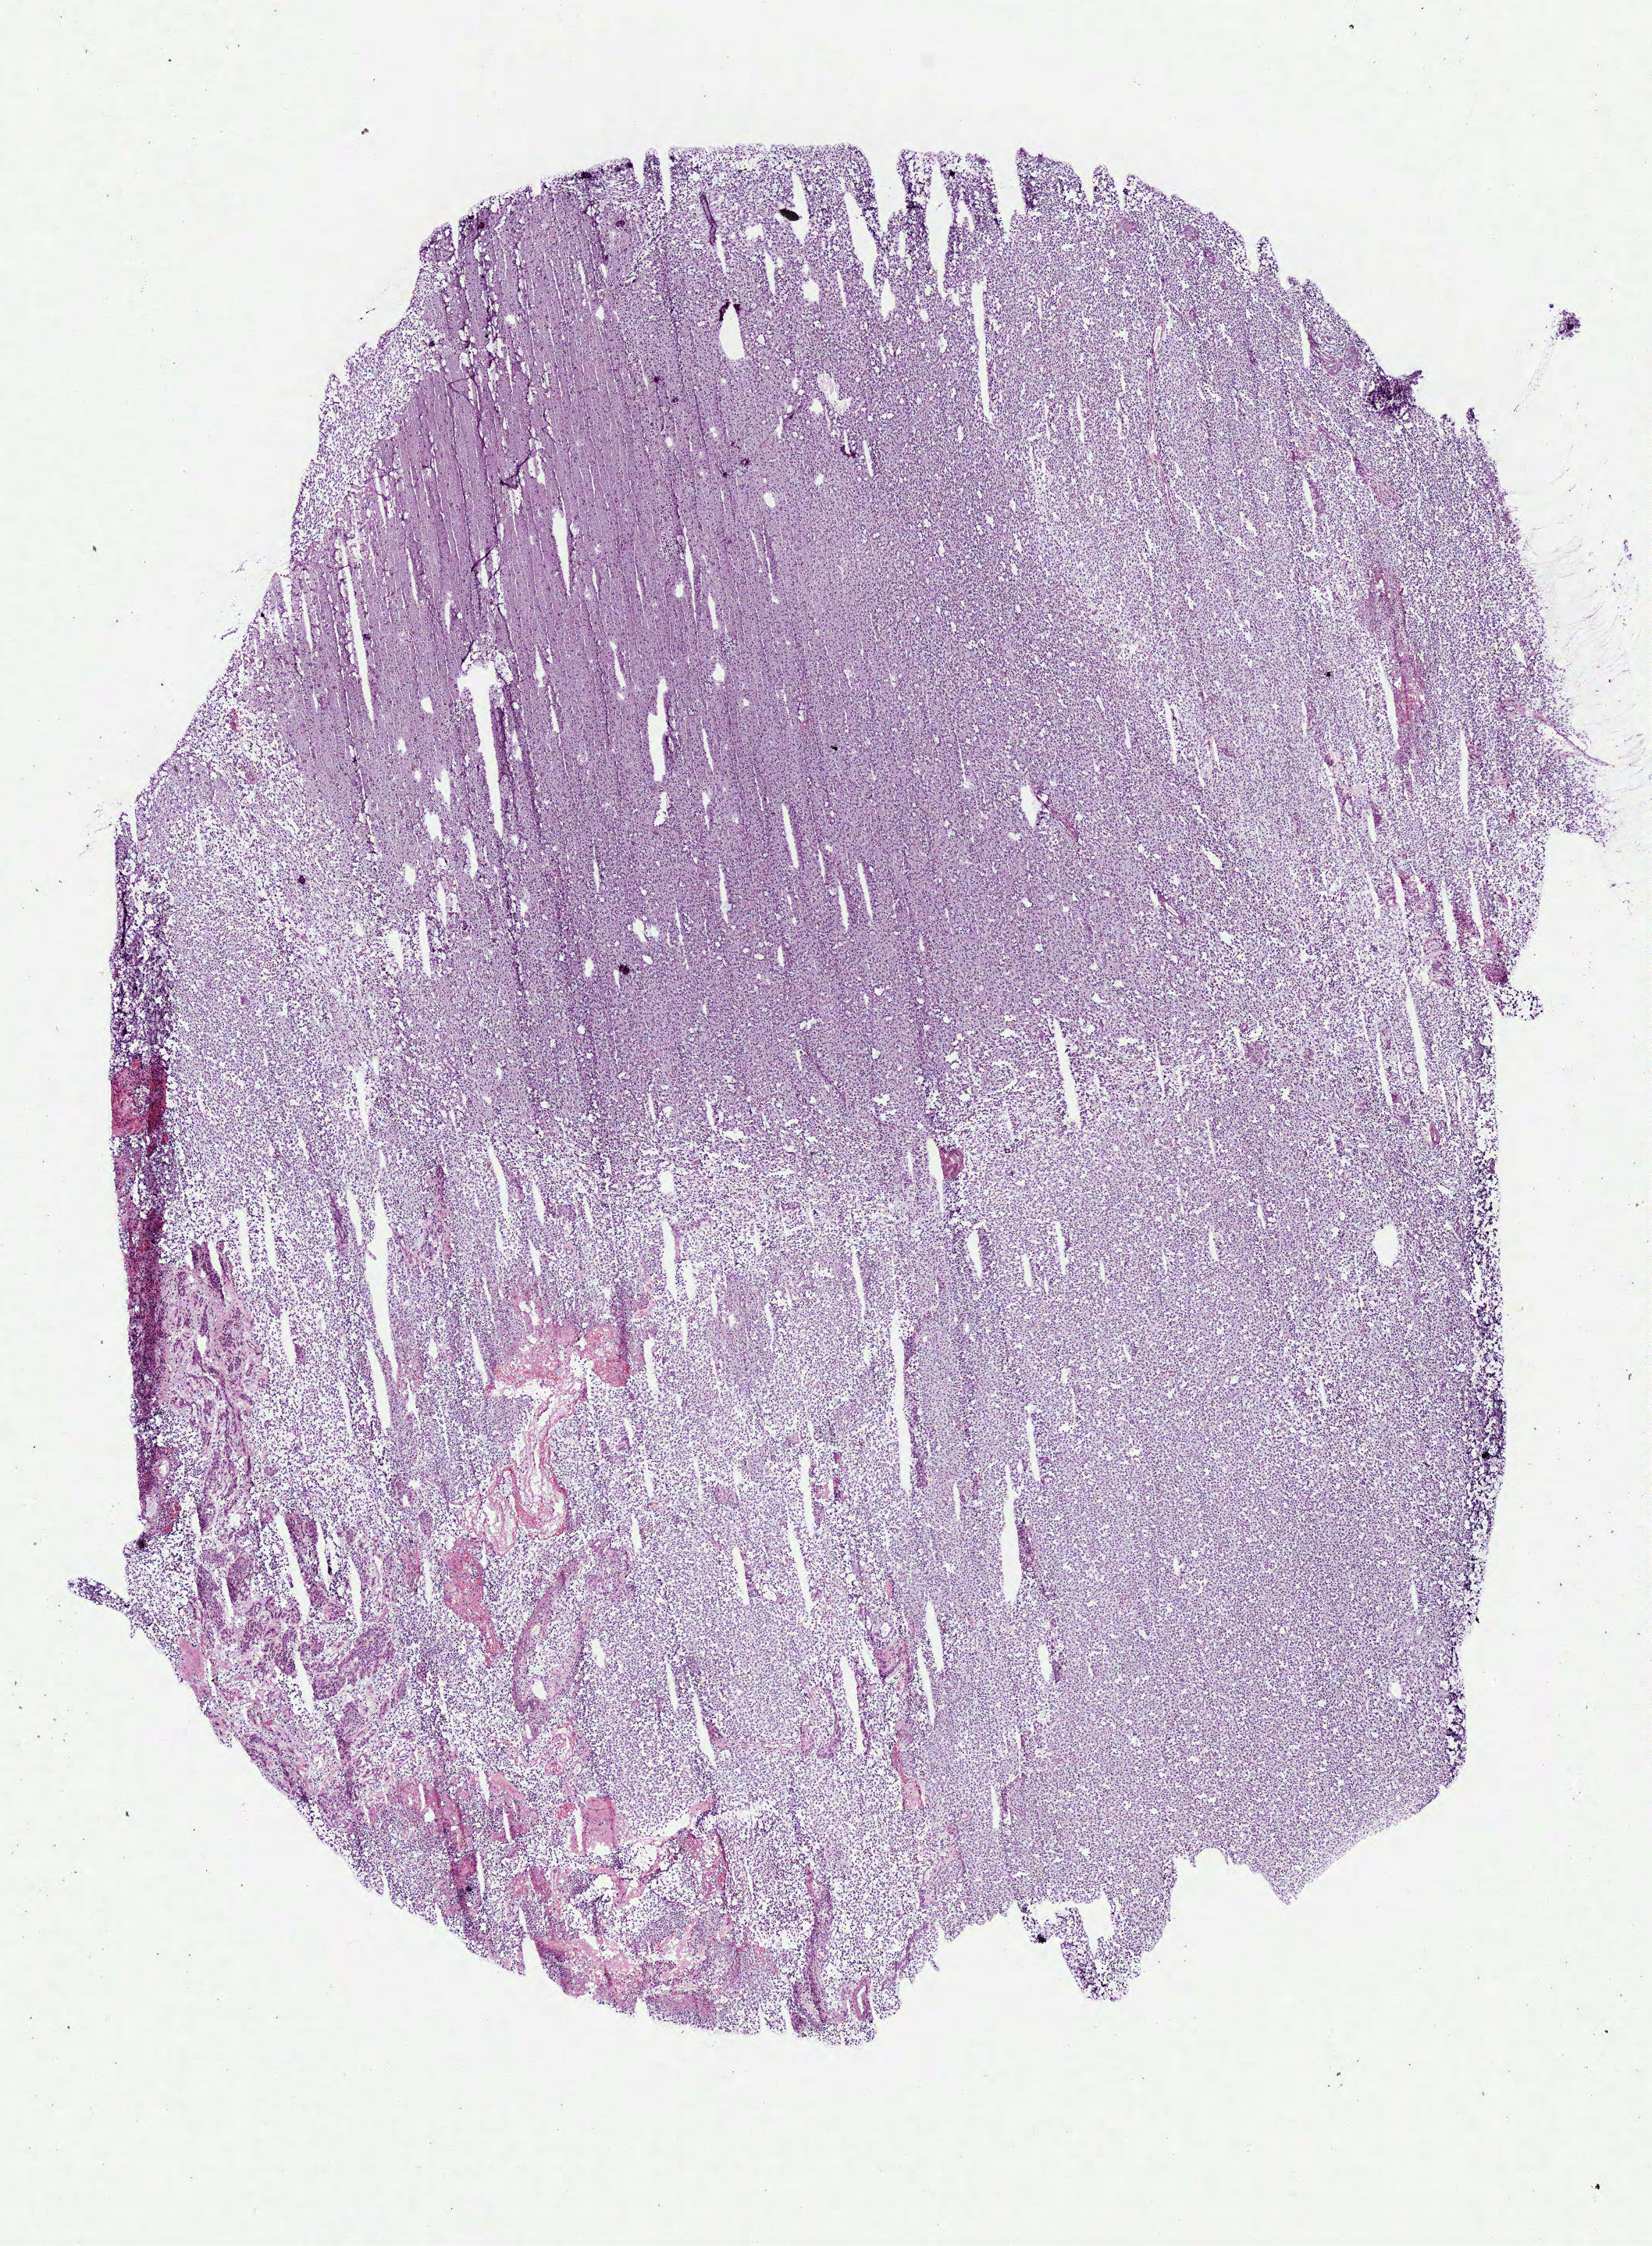
Whole-slide histology image, Hematoxylin and eosin (H&E) stained, a low-resolution overview of the entire scanned area, about 8.3 x 11.3 mm (slide scanned at 40x), frozen section from the bottom of the tissue portion, brain, primary tumour sample. Male, age 56 years at initial diagnosis. Histologic grade: G3 (poorly differentiated). Composition of this section per pathologist review: tumour cells 100%, tumour nuclei 80%, normal cells 0%, stromal cells 0%, necrosis 0%.
Histologic diagnosis: Oligodendroglioma, anaplastic (cerebrum). Laterality: midline.